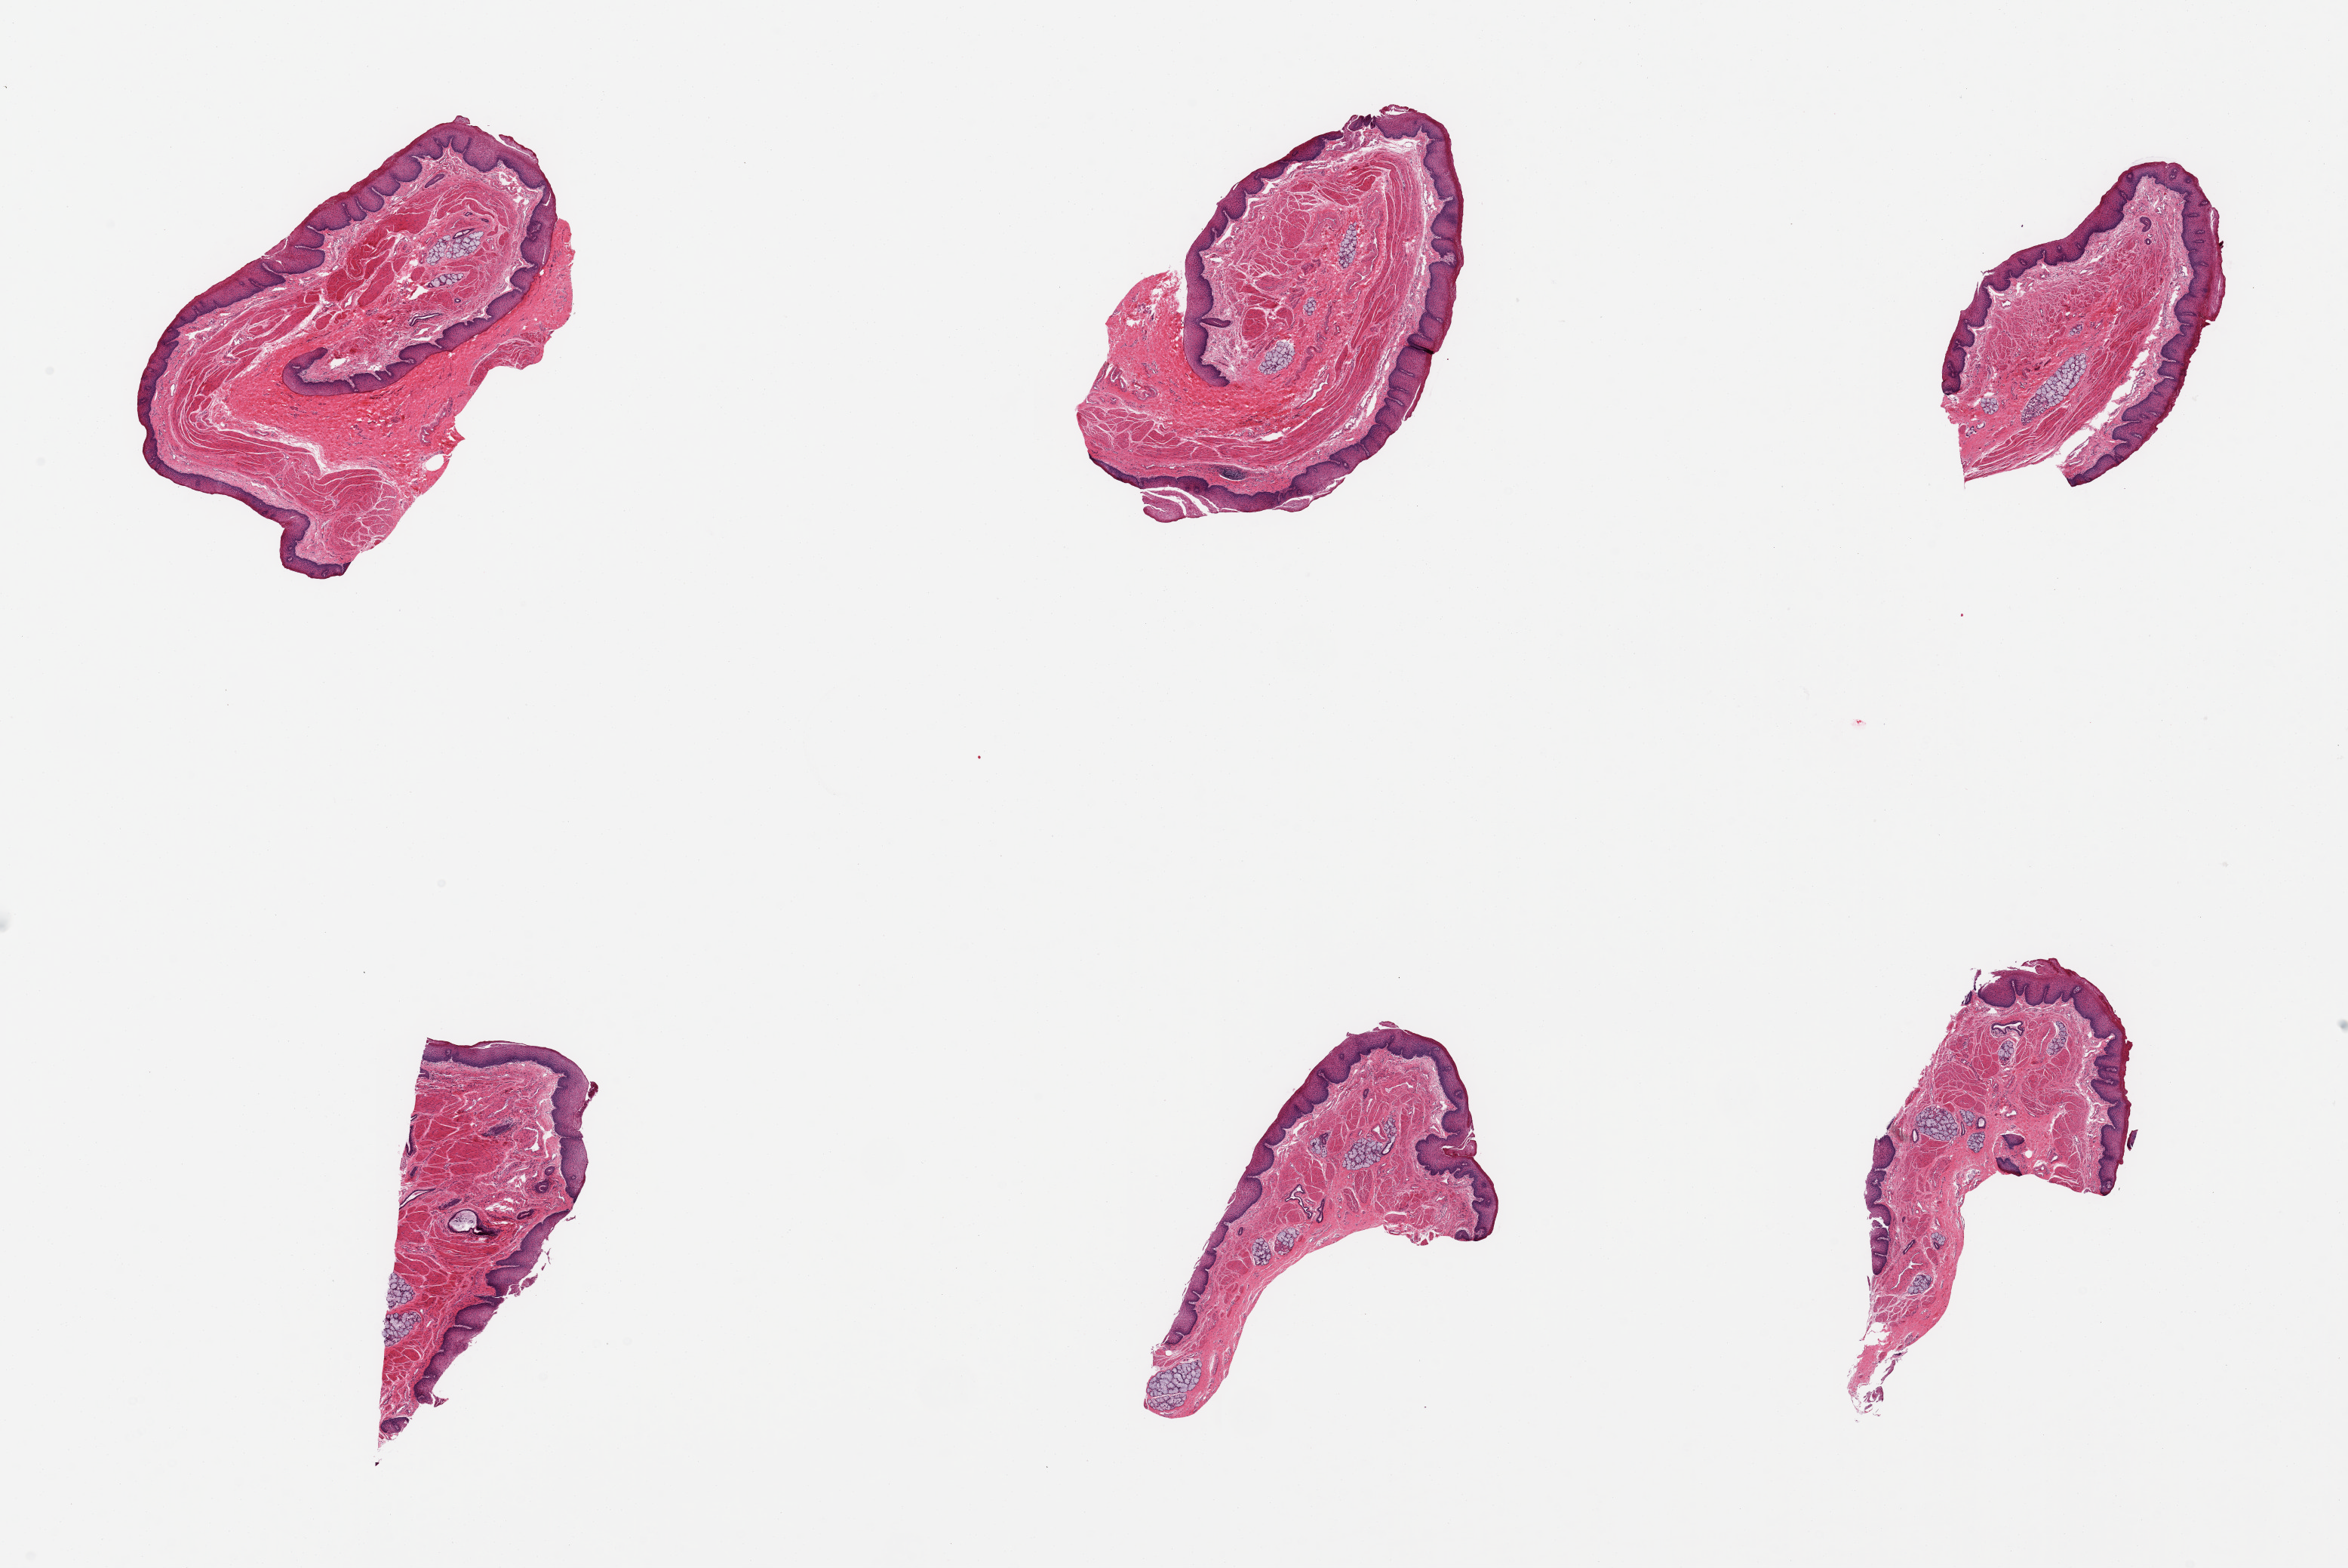
Haematoxylin and eosin whole-slide image, a low-resolution overview of the entire scanned area, about 24.6 x 16.4 mm, PAXgene-fixed paraffin-embedded (PFPE) section, target tissue: esophageal mucous membrane, tissue donor sample. Female donor.
• pathologist's review note for this sample: 6 pieces; numerous submucosal glands